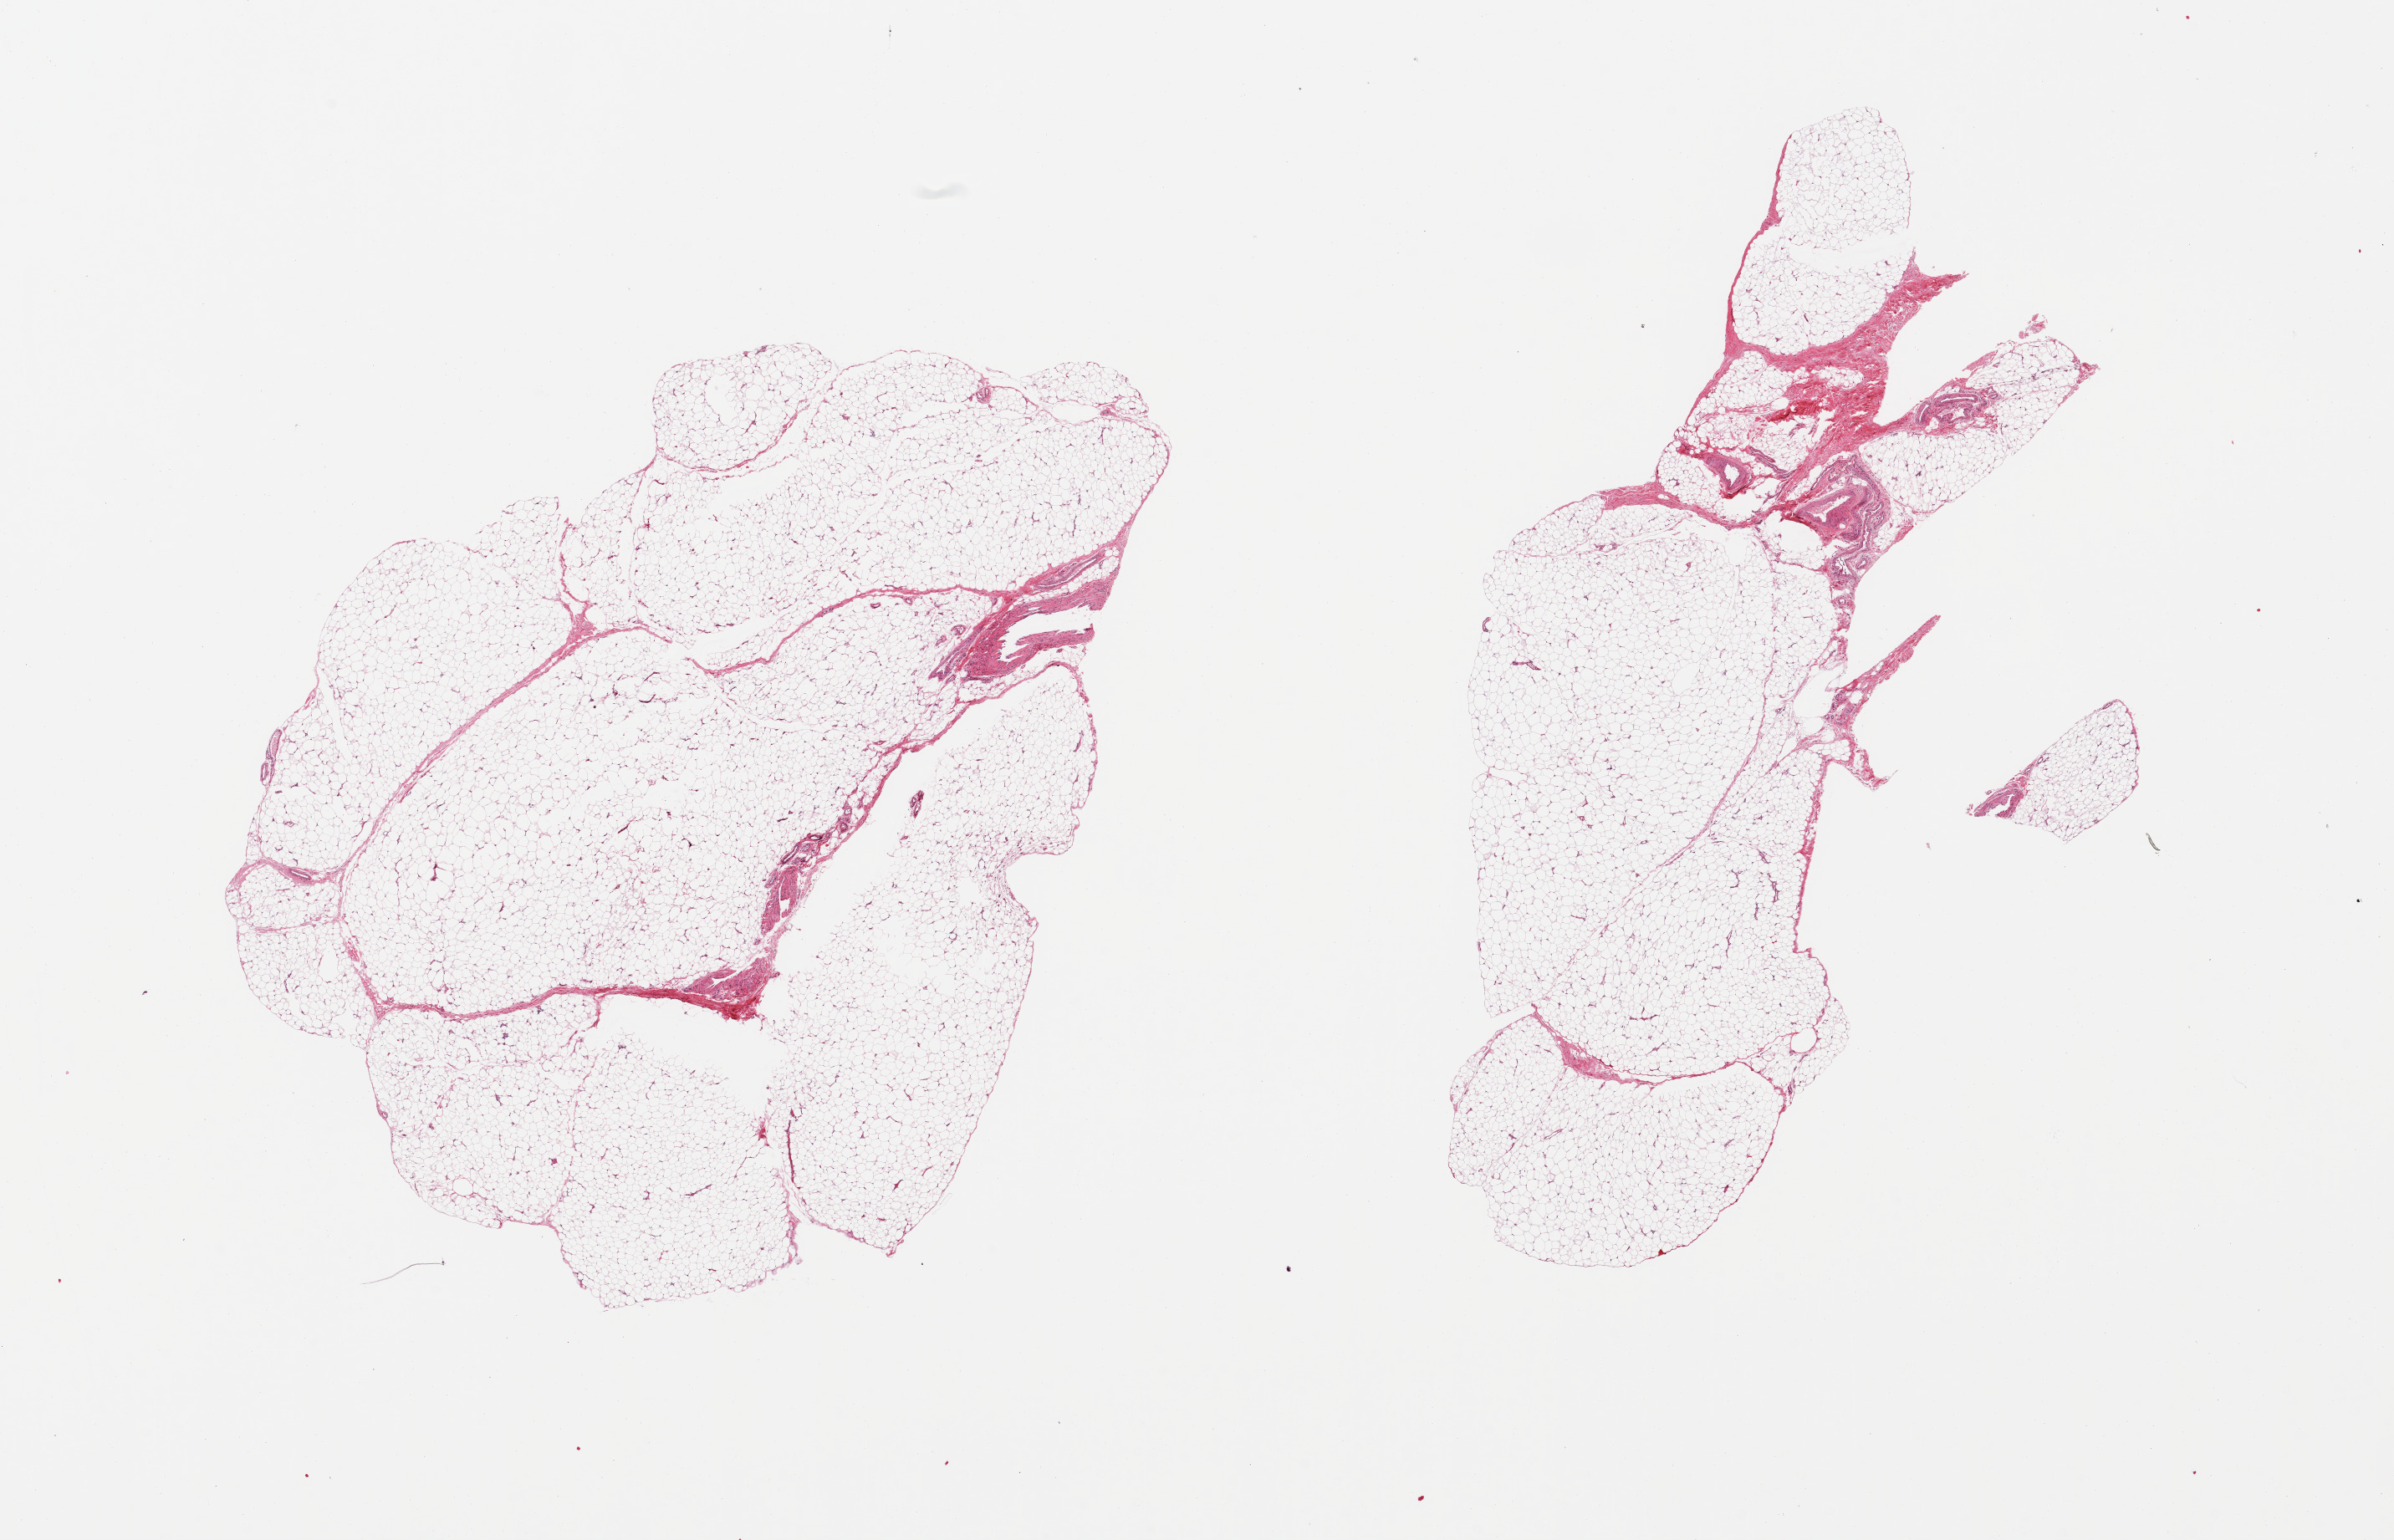
H&E whole-slide image, shown as a low-resolution overview of the whole scanned area (about 22.6 x 14.6 mm, slide scanned at 20x); PAXgene-fixed paraffin-embedded (PFPE) section; target tissue: adipose tissue; donor tissue sample. Donor: female.
• reviewer comment on this tissue sample: 2 pieces, fascia is ~10%